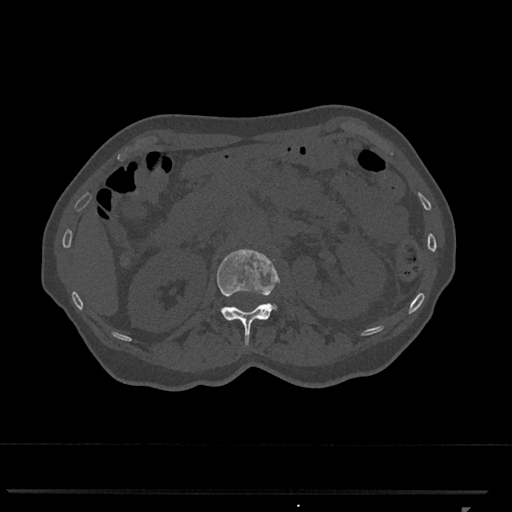
CT including the spine, one axial slice; position 397 of 793 along the scan axis; bone window (W 1800 / L 400 HU); 0.5 mm slice thickness; 512 × 512 image matrix, field of view 380 × 380 mm. Female patient, age 62 years. Case-level facts recorded for this patient, not image findings: primary cancer: renal.
Outlined on this slice (semi-automatic segmentation, software-assisted and operator-edited):
- L1 vertebra: bounding box (x1, y1, x2, y2) in pixels: (217, 249, 280, 346)